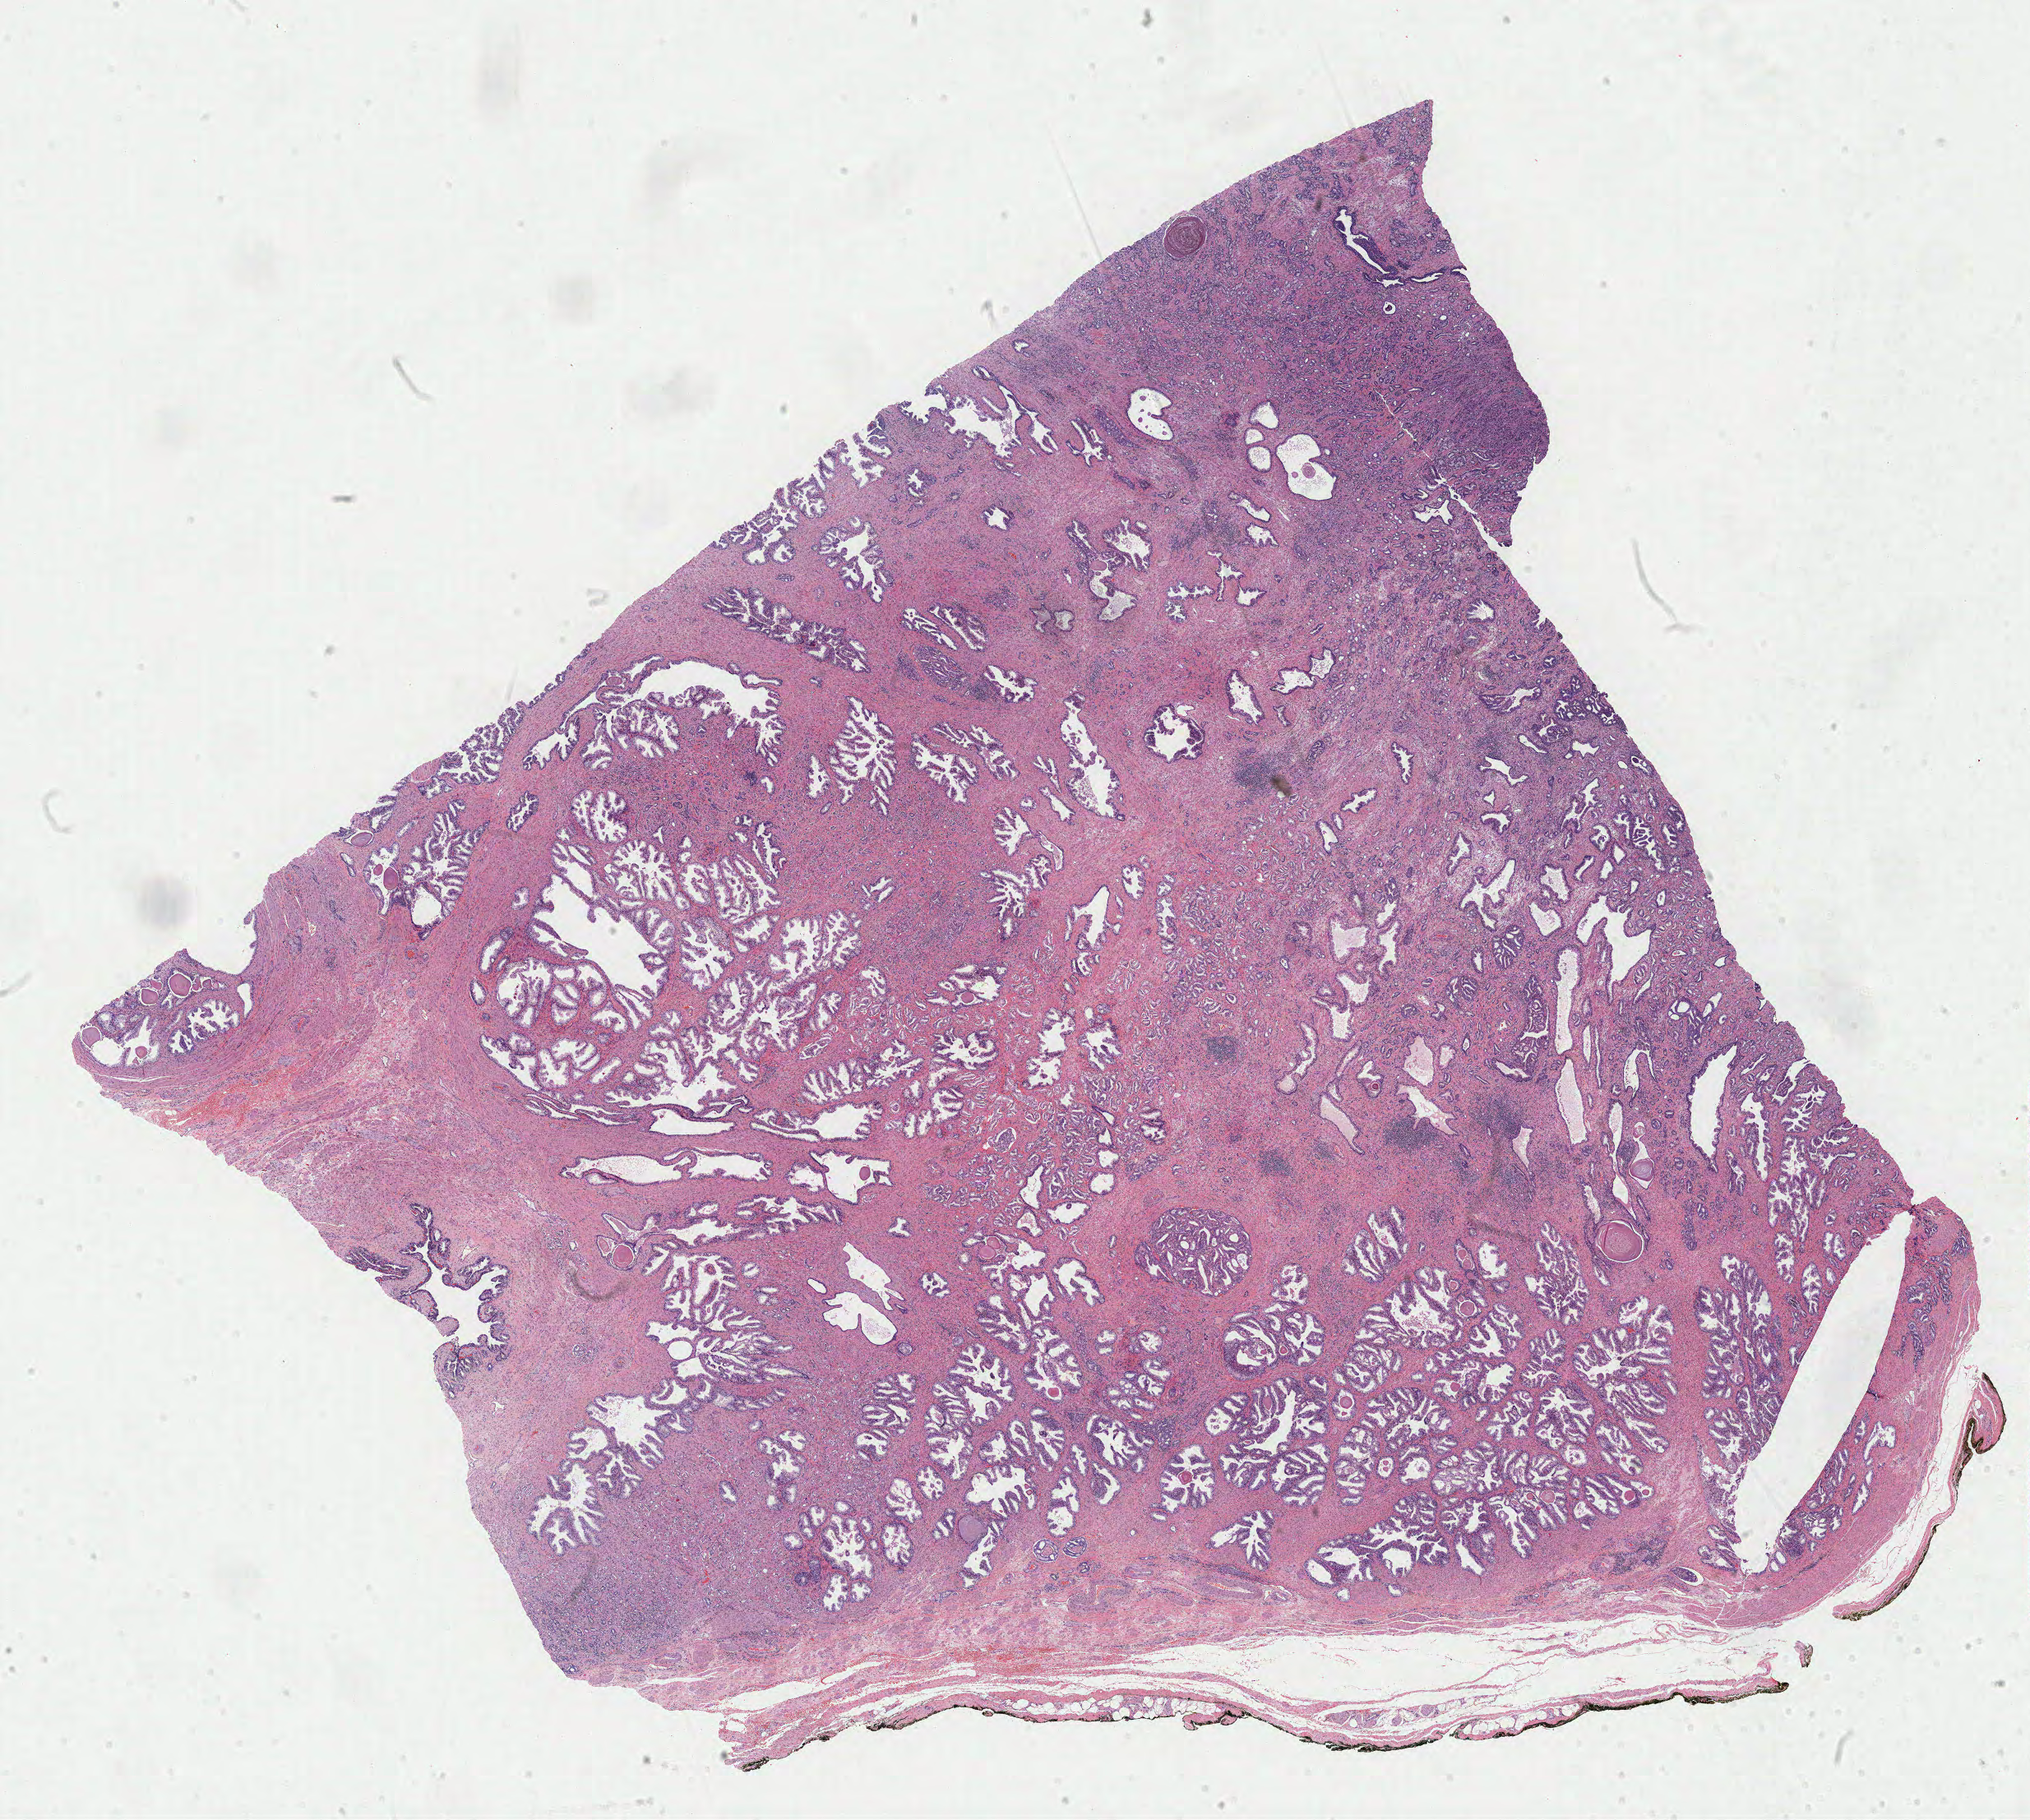
Whole-slide histology image, H&E — whole scanned area (about 19.6 x 17.6 mm, from a 40x scan) shown as a low-resolution overview; formalin-fixed paraffin-embedded (FFPE) diagnostic section; primary tumour sample from the prostate. Male patient; age at initial diagnosis 69 years. Gleason score: 9 (4+5).
Pathologic diagnosis: Adenocarcinoma, NOS (prostate gland).